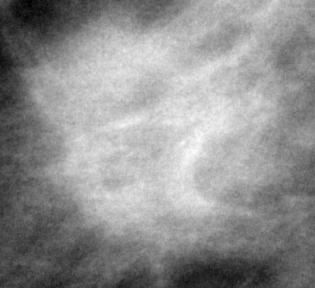
Cropped region of a digitized screen-film mammogram centred on a radiologist-marked abnormality, right breast, CC view.
- Finding: mass, shape lobulated, margins ill defined; BI-RADS assessment category 4; pathology (as recorded): malignant.